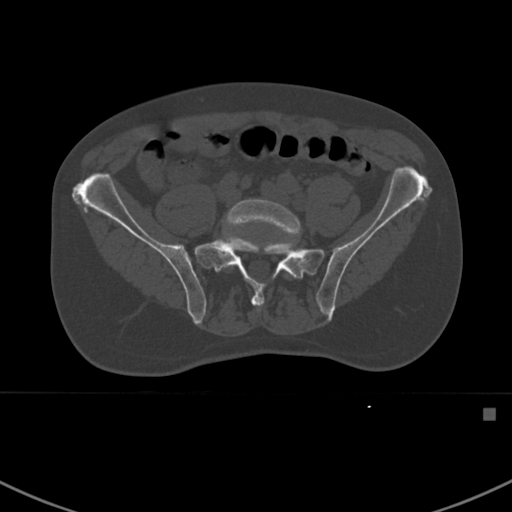
CT including the spine, one axial slice. Slice 208 of 412 in the series (ordered by position). 120 kVp. Bone window (W 1800 / L 400 HU). 1.5 mm slice thickness. 512 × 512 image matrix, field of view 358 × 358 mm. Male patient, age 59 years. From the clinical record (not read from this slice): primary cancer: prostate.
Outlined on this slice (semi-automatic segmentation, software-assisted and operator-edited):
- L5 vertebra: box from (x=224, y=199) to (x=301, y=275) px